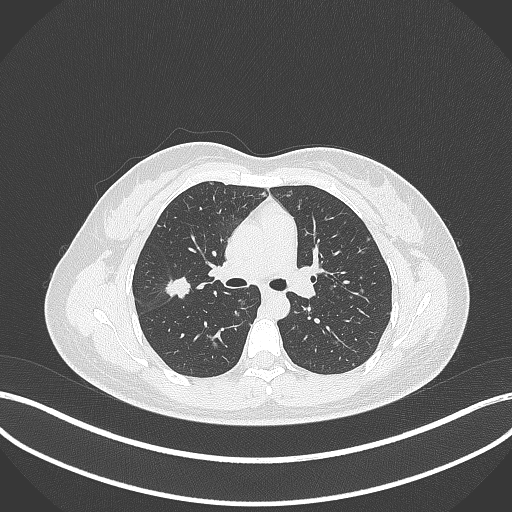
Chest CT, one axial slice. Position 206 of 307 along the scan axis. Lung window (W 1500 / L -600 HU). 1 mm slice thickness. 512 × 512 image matrix, field of view 400 × 400 mm. Patient: female, 33 years. Case-level facts recorded for this patient, not image findings: clinical TNM (as recorded): T1c N0 M0; histopathological grade: G2-G3.
Annotated regions visible in this slice (rectangle marked by the reading radiologist):
- lung tumour (recorded histology: adenocarcinoma): box from (x=165, y=274) to (x=194, y=303) px